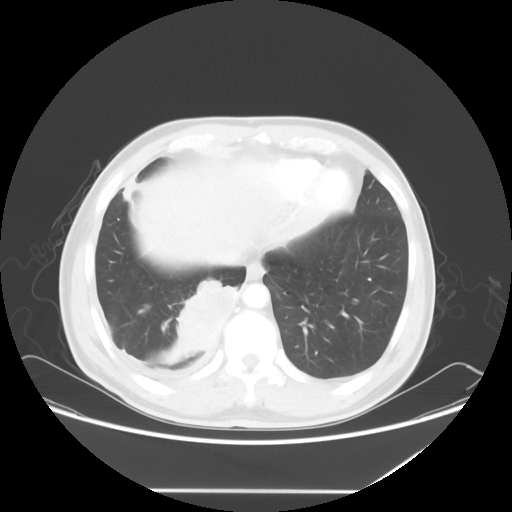
Chest CT, one axial slice; slice 15 of 60 in the series (ordered by position); lung window (W 1500 / L -600 HU); 512 × 512 image matrix. Patient: male, 48 years. From the clinical record (not read from this slice): clinical TNM (as recorded): T3 N3 M1a.
Annotated regions visible in this slice (bounding box drawn by a radiologist):
- lung tumour (recorded histology: squamous cell carcinoma): bounding box [x1, y1, x2, y2] px = [170, 265, 241, 357]